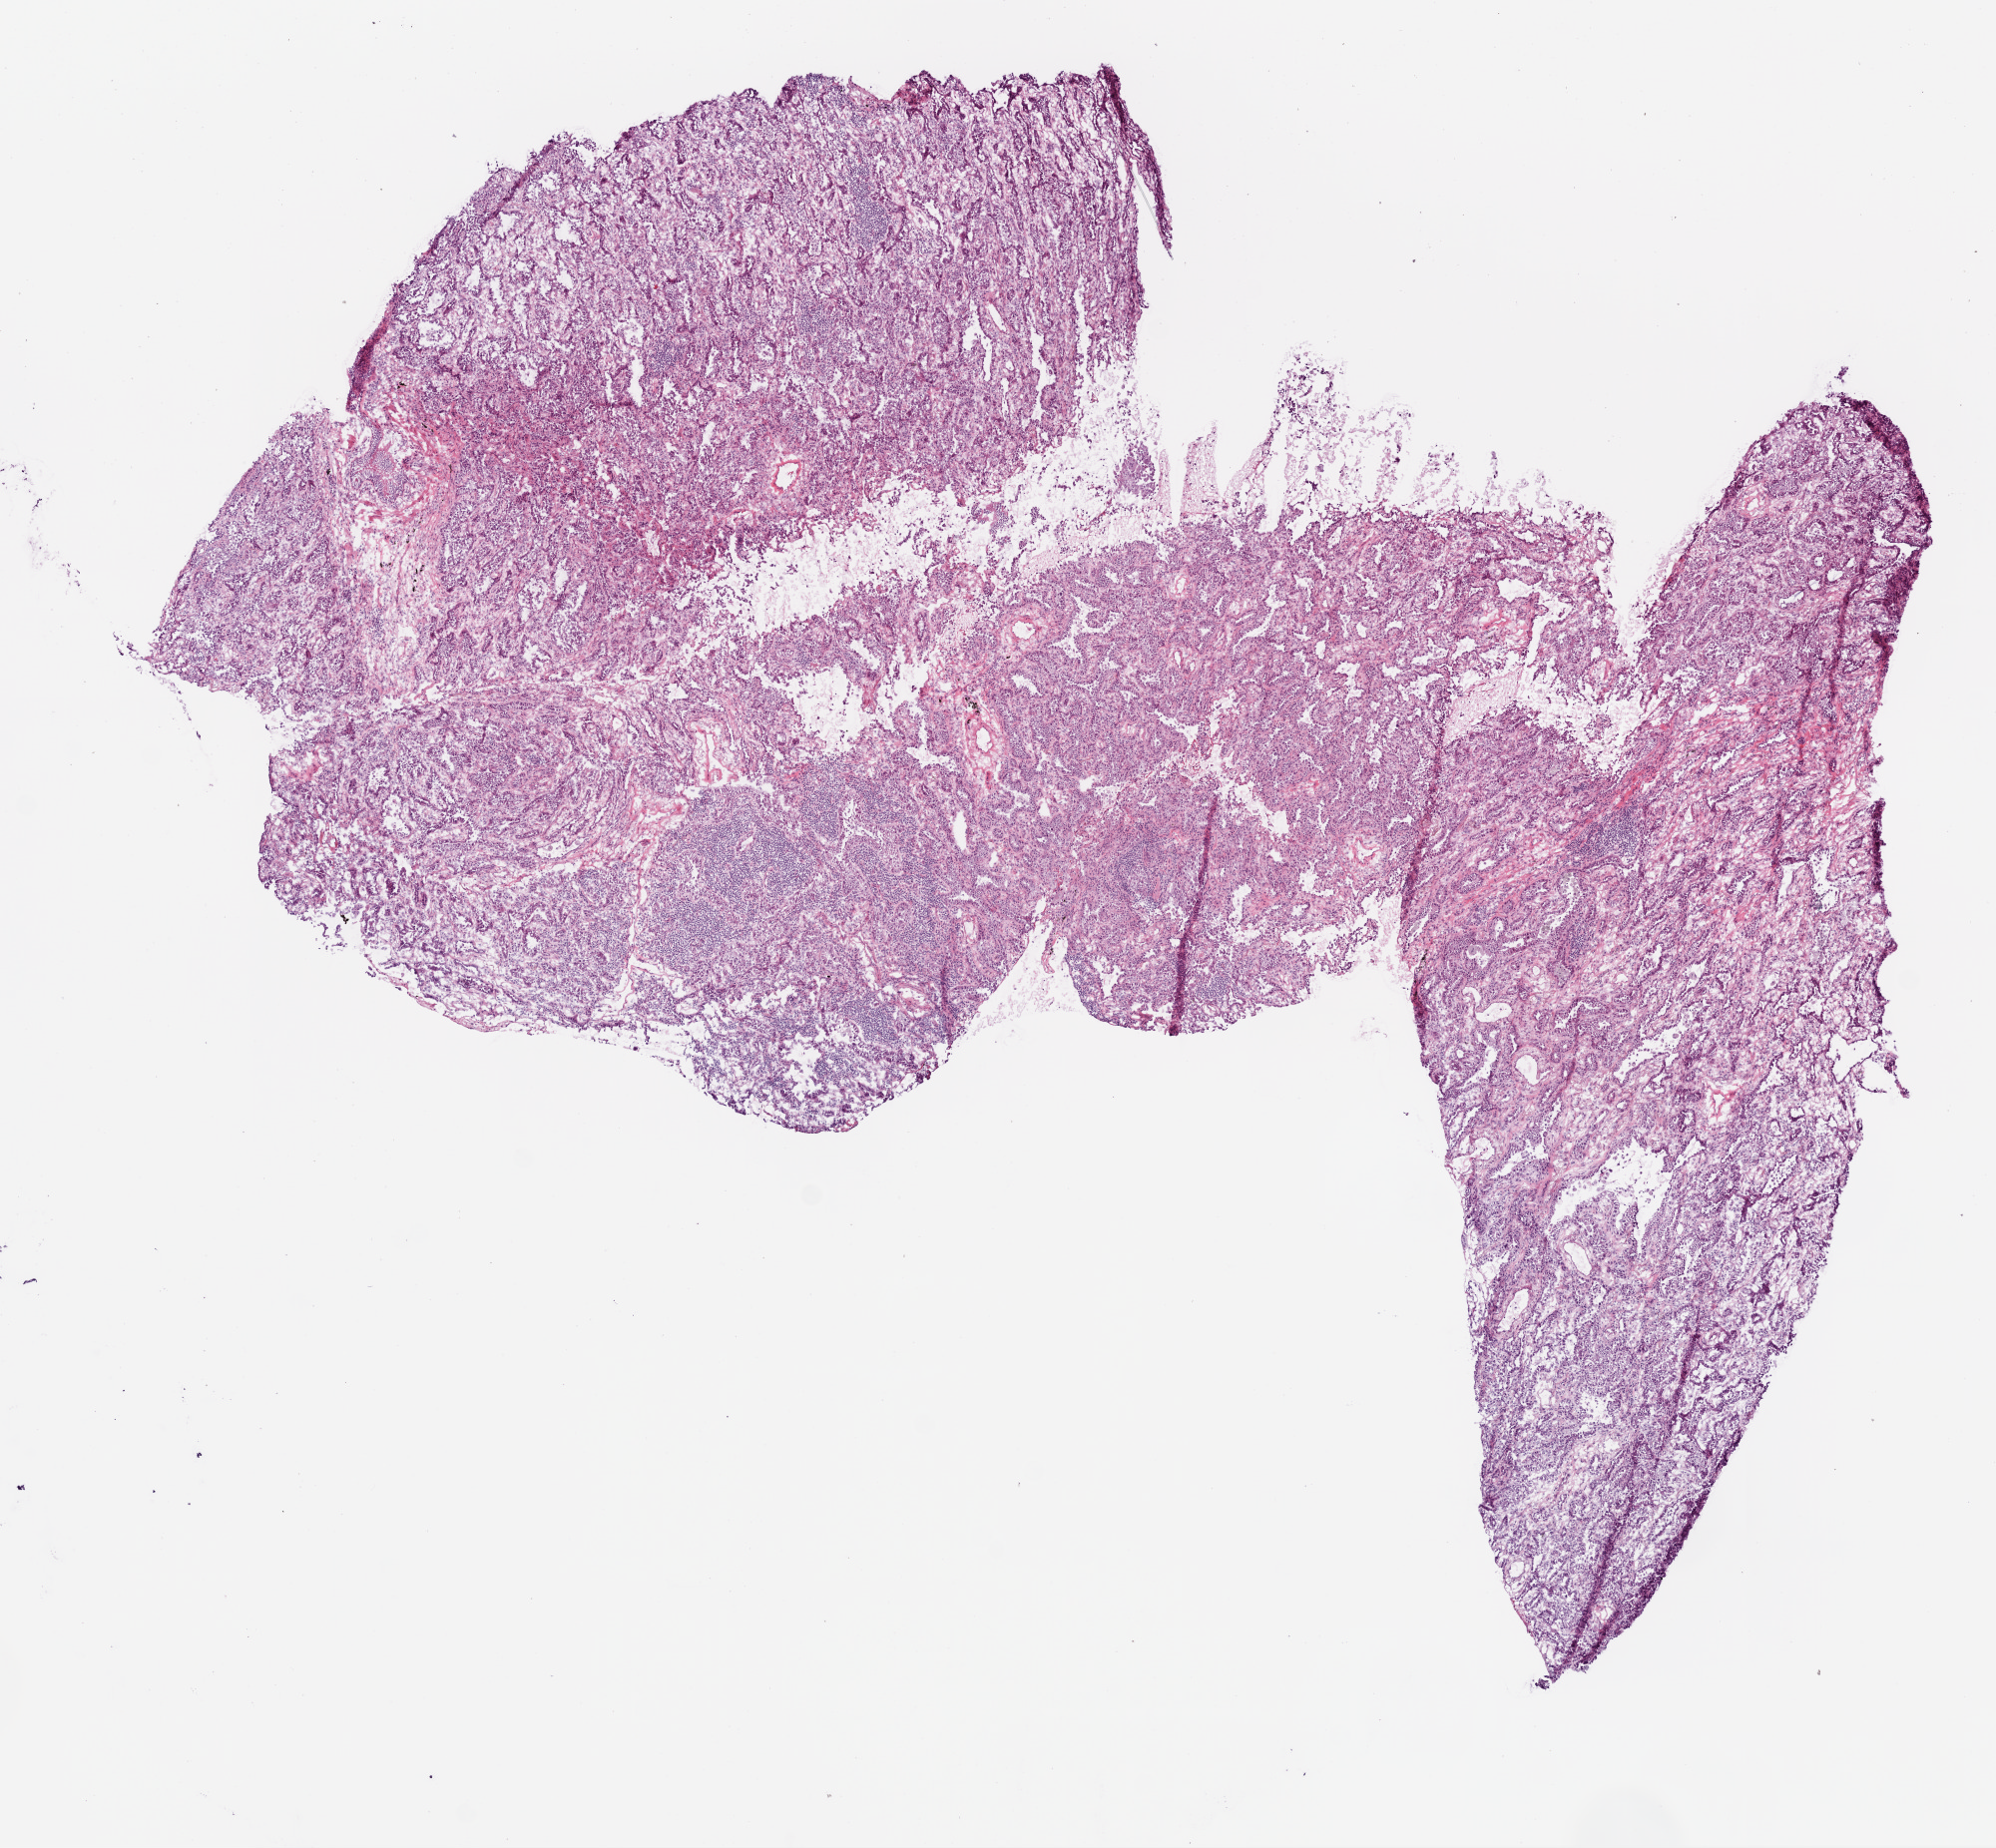
Digitized H&E tissue section (whole slide) — shown as a low-resolution overview of the whole scanned area (about 8.0 x 7.4 mm, slide scanned at 20x), frozen section from the bottom of the tissue portion, primary tumour sample from the lung. Male patient. Pathologist review of this section (percent, as recorded): tumour cells 90%, tumour nuclei 60%, normal cells 0%, stromal cells 10%, necrosis 0%.
AJCC pathologic stage: IB (6th edition). Histologic diagnosis: Bronchiolo-alveolar carcinoma, non-mucinous (lower lobe, lung).